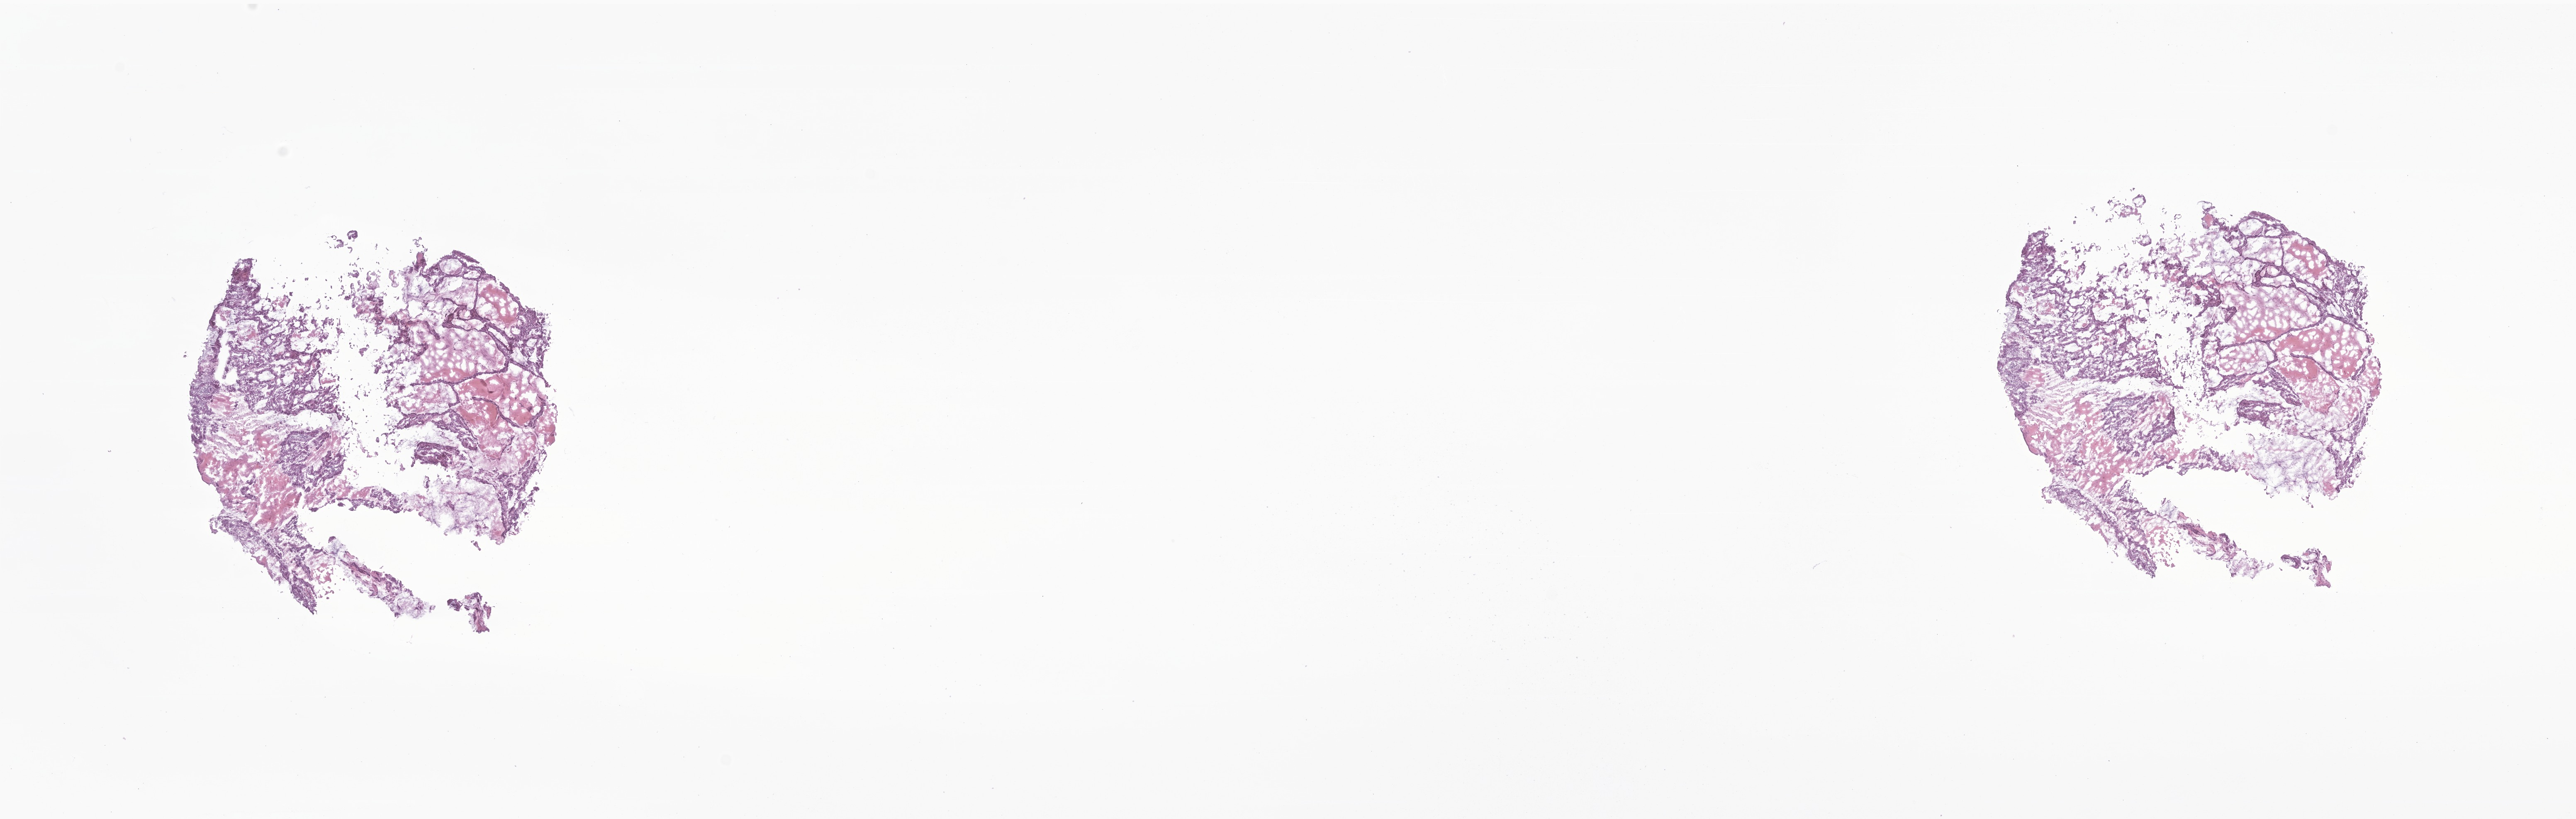
Digitized H&E-stained section of tumor tissue from the lung — low-resolution overview of the scanned area, about 26.2 x 8.3 mm; cryosection (OCT / tissue freezing medium). Patient male; age 157 months.
Diagnosis (ICD-O-3 morphology term): Carcinoma, NOS.